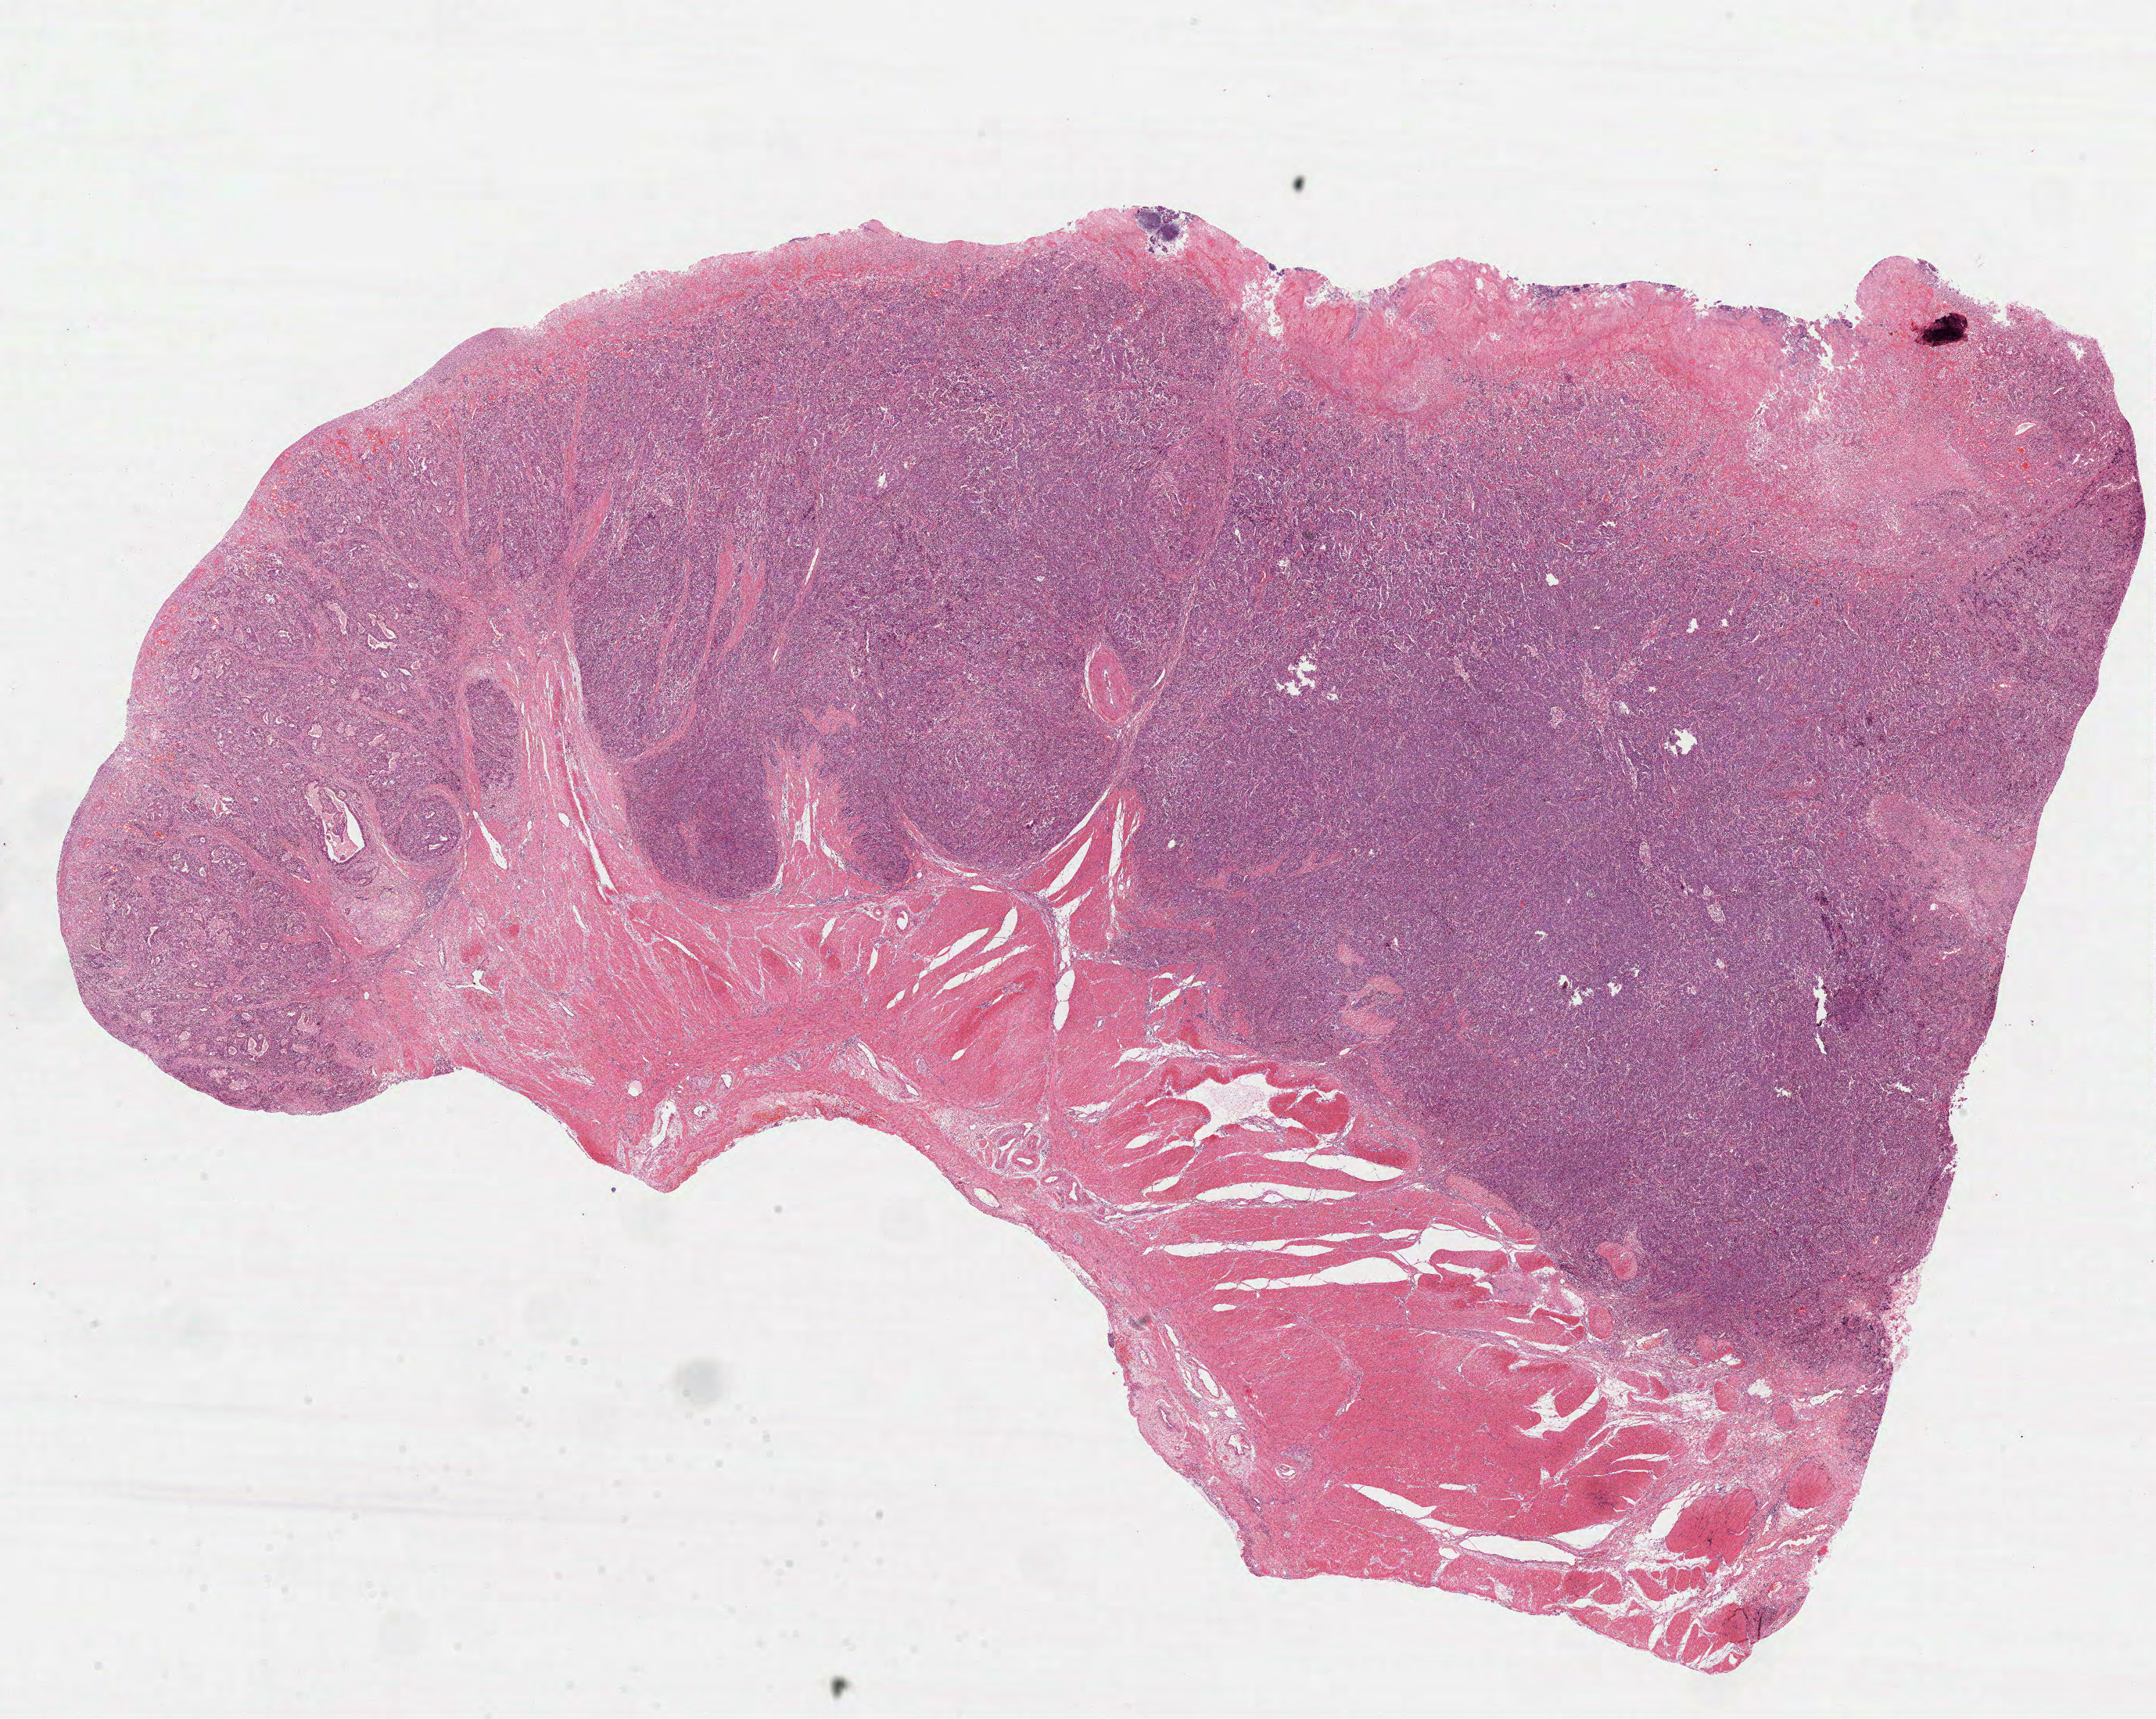
Whole-slide histology image, Hematoxylin and eosin (H&E) stained — a low-resolution overview of the entire scanned area, about 22.2 x 17.7 mm (slide scanned at 40x). FFPE section. Primary tumour sample from the stomach. Male, age 59 years at initial diagnosis. Histologic grade: G3 (poorly differentiated).
AJCC pathologic stage: IIIB (7th edition). Histologic diagnosis: Adenocarcinoma, intestinal type (gastric antrum).